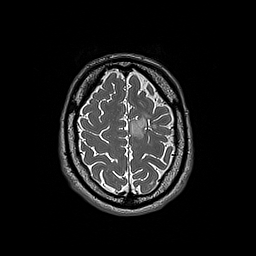
Brain MRI from a brain-tumour surgery series, one axial slice. 1 mm slice thickness. 256 × 256 image matrix, field of view 250 × 250 mm. From the clinical record (not read from this slice): histopathology: Oligodendroglioma; WHO grade: 3; IDH mutation: yes.
Structures marked on this image (outlined manually by an expert reader):
- tumour: box from (x=130, y=112) to (x=155, y=138) px